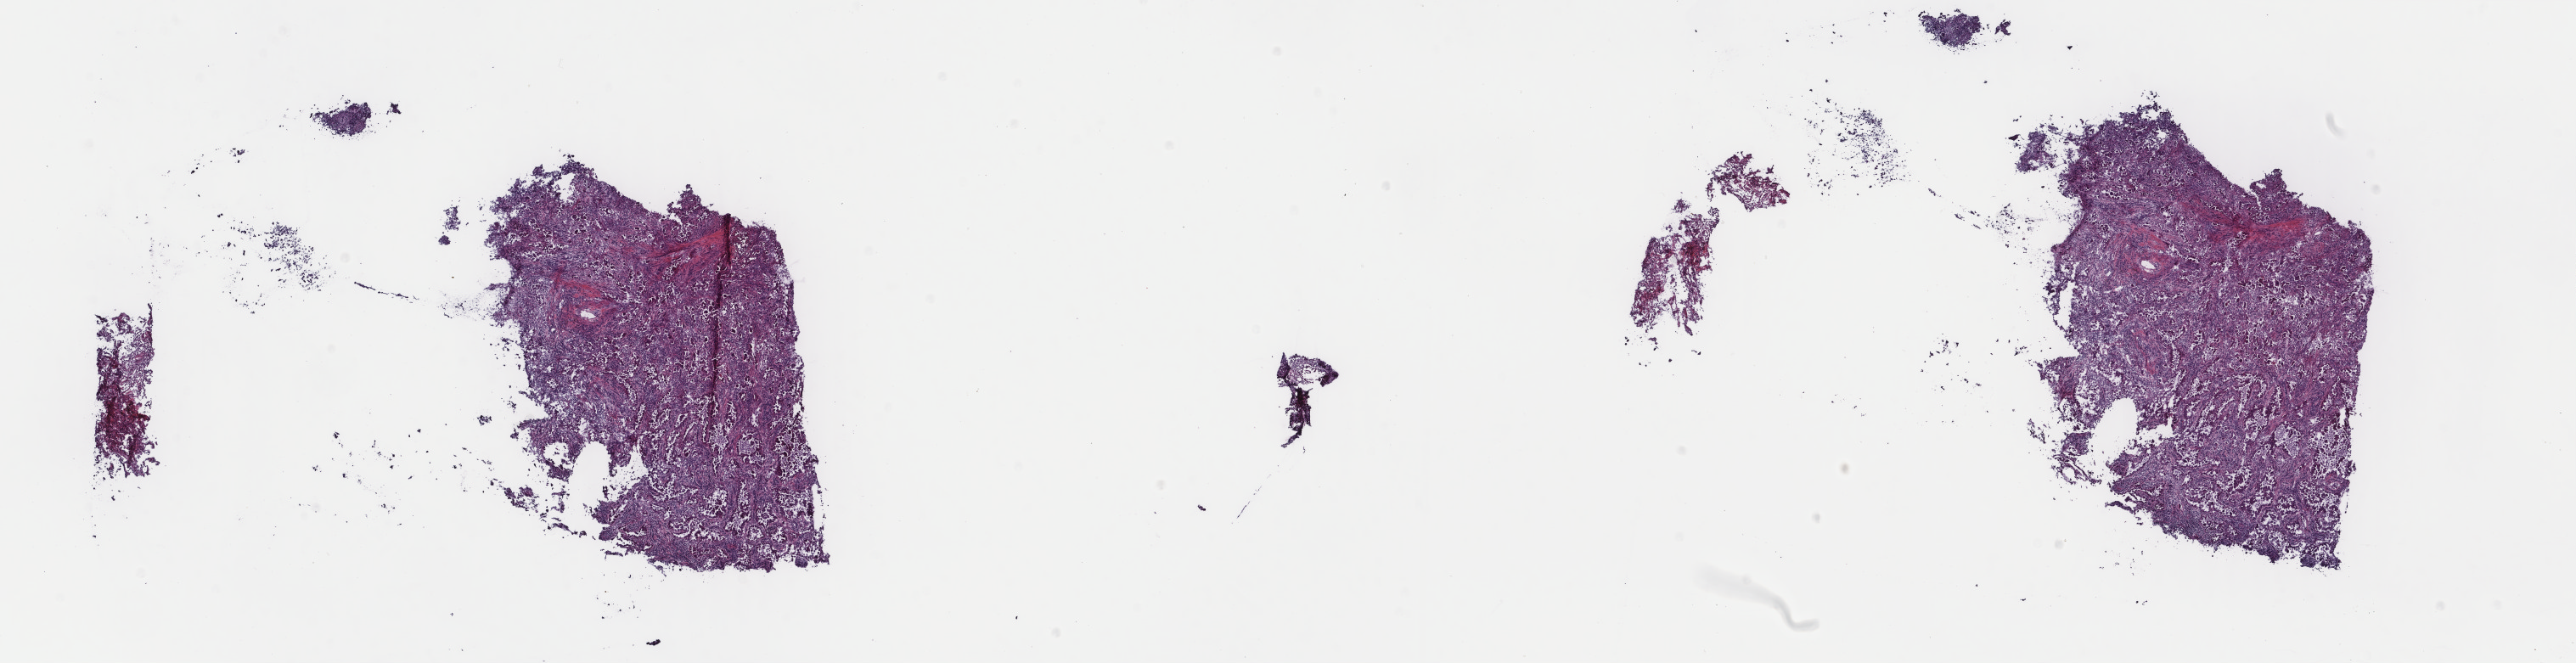
Digitized H&E-stained tissue section (whole slide) — a low-resolution overview of the entire scanned area, about 24.1 x 6.2 mm. Frozen section. Lung, primary tumour sample. Female, age 60 years at initial diagnosis. Pathologist review of this section (percent, as recorded): tumour cells 50%, tumour nuclei 60%, normal cells 0%, stromal cells 50%, necrosis 0%. Inflammatory infiltration, as recorded: lymphocyte infiltration 10%, monocyte infiltration 15%, neutrophil infiltration 1%.
- pathologic diagnosis: Squamous cell carcinoma, NOS (upper lobe, lung)
- laterality: left
- AJCC pathologic stage: IA (7th edition)